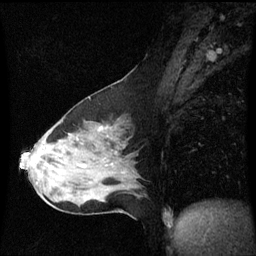
Breast MRI (dynamic contrast-enhanced), one sagittal slice. Position 33 of 60 along the scan axis. Dynamic contrast-enhanced series, image 2 of 3 at this slice position (ordered by acquisition). 1.5 T. TE 4.2 ms, TR 8.9 ms. 256 × 256 image matrix, field of view 210 × 210 mm. Patient: female, 50 years. From the clinical record (not read from this slice): setting: breast cancer imaged before/during neoadjuvant chemotherapy; receptor status: HR-positive, HER2-negative.
Structures marked on this image (semi-automatically segmented with operator editing):
- analysis volume of interest (the breast-tissue region the enhancement analysis was run in; not a lesion): bounding box [x1, y1, x2, y2] px = [20, 98, 142, 210]
- tumour enhancement mask (voxels above the 70 % enhancement threshold inside the analysis volume of interest): [101, 128, 103, 131]